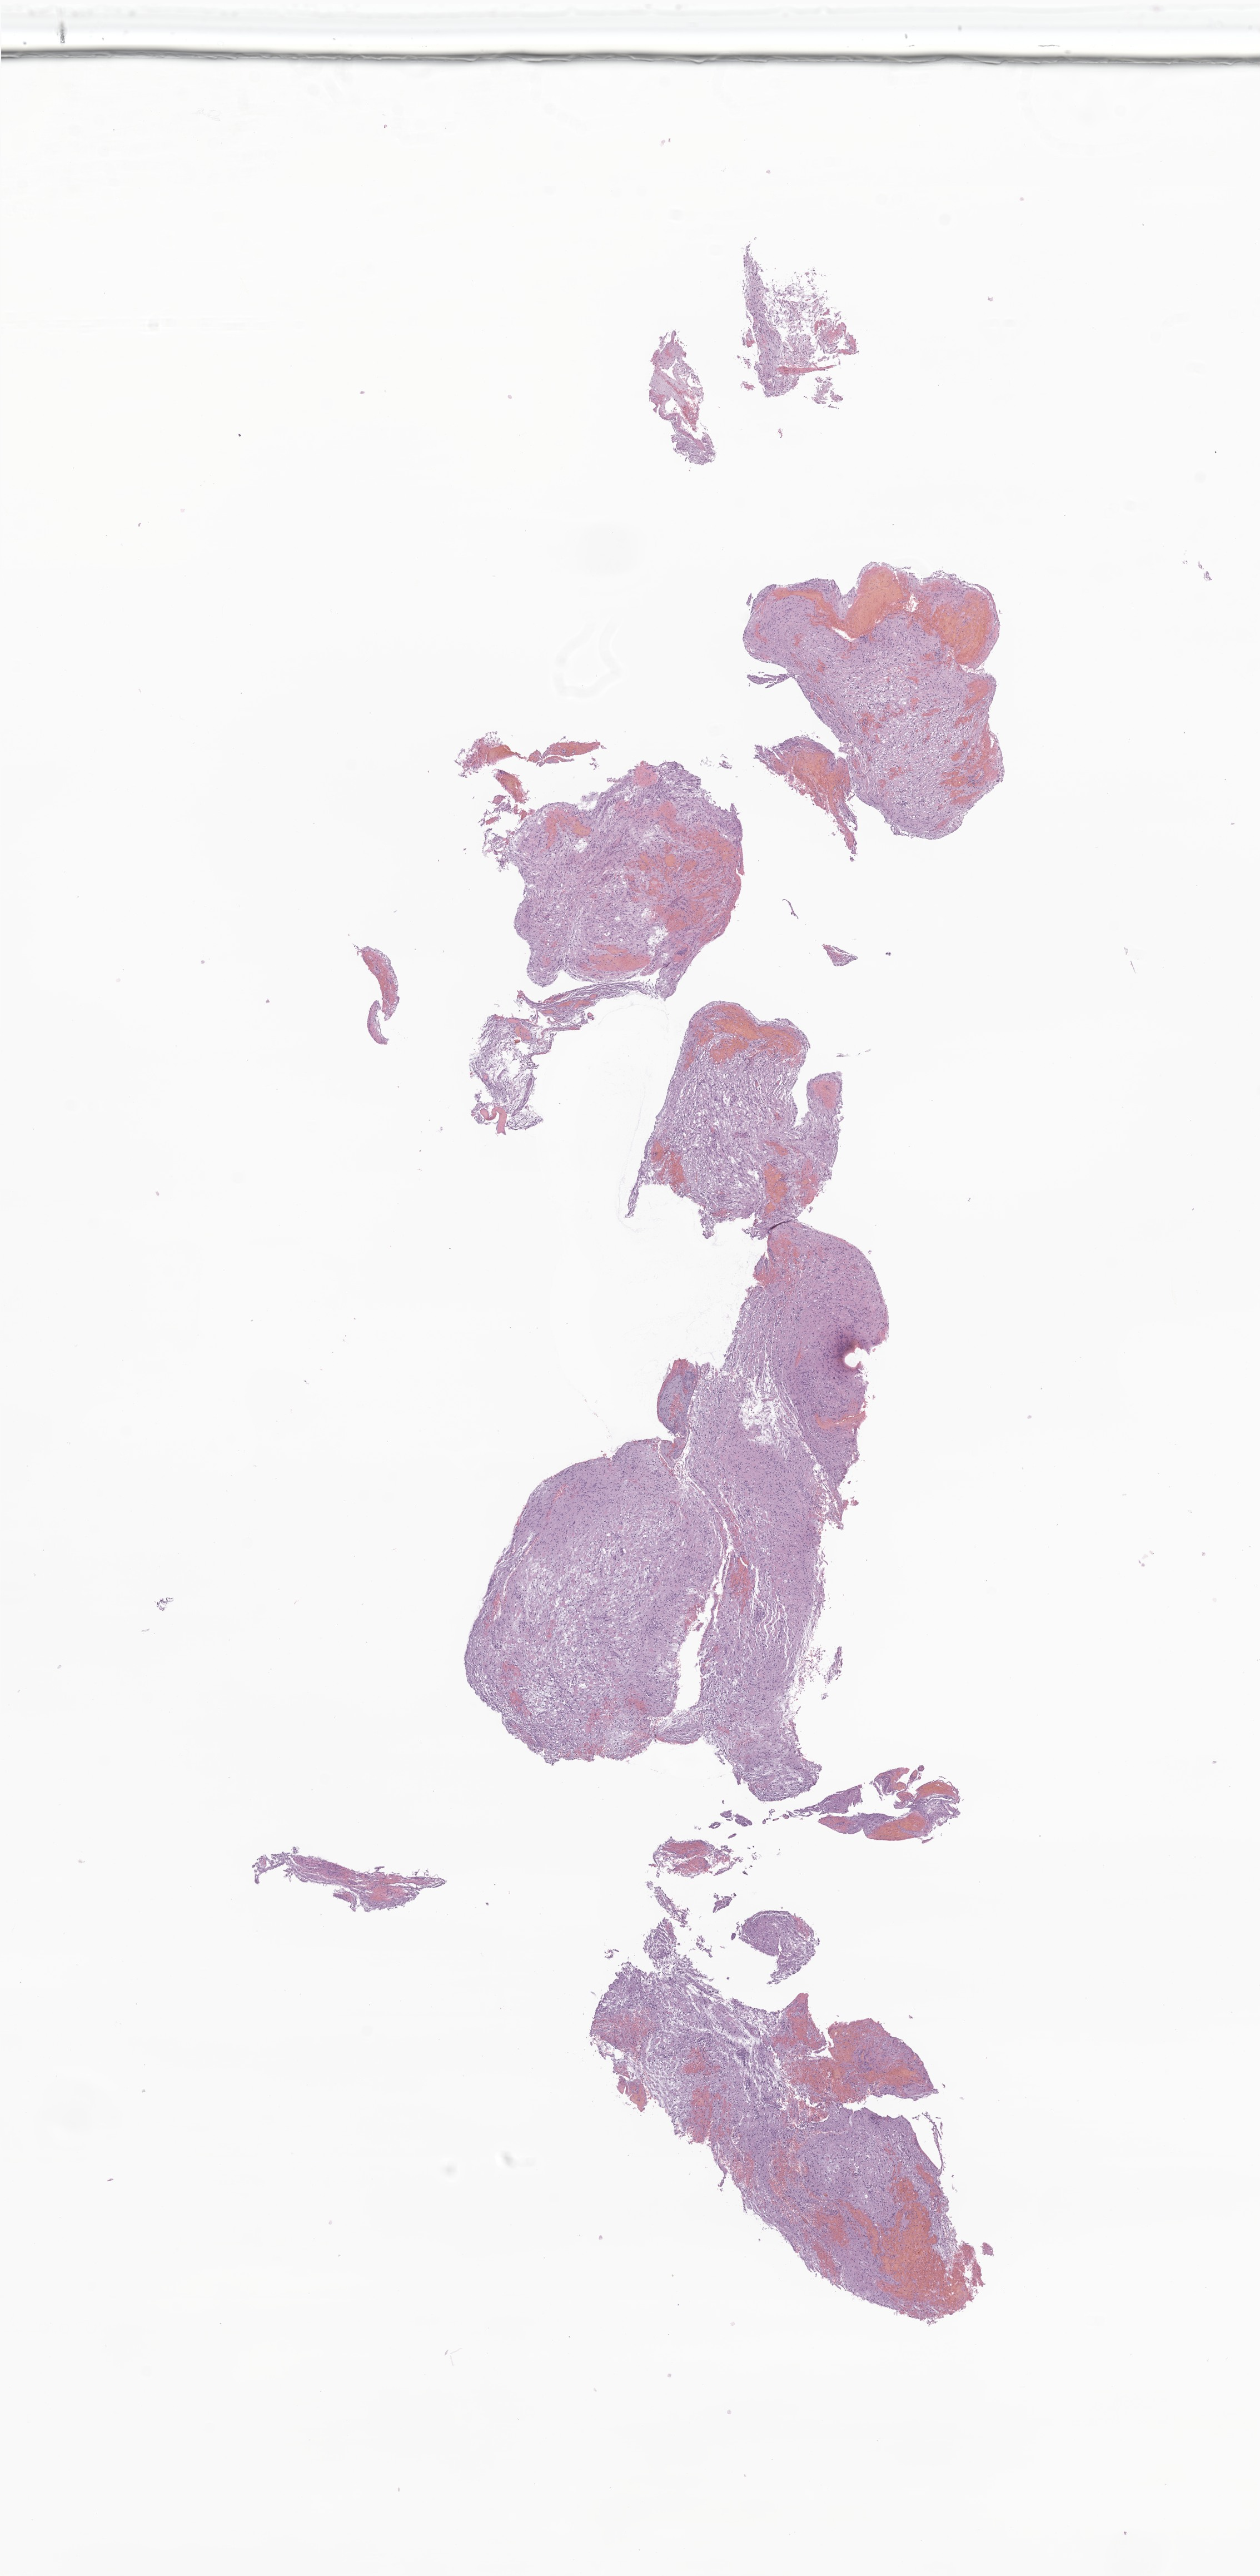
H&E whole-slide image of tumor tissue from the brain — shown as a low-resolution overview of the whole scanned area (about 9.6 x 19.5 mm); FFPE section. Female patient, age 169 months (14 years 1 month).
Recorded diagnosis: Oligoastrocytoma, NOS.